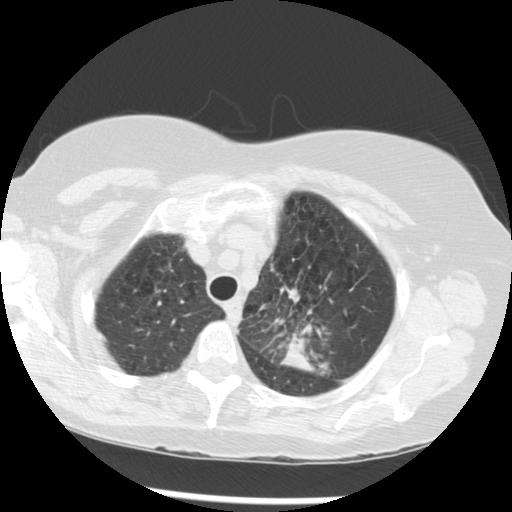
Low-dose screening chest CT, axial slice. Third annual screen. Lung window (W 1500 / L -600 HU). Slice 233 of 283 in the series. Female participant, aged 70 years at enrolment. Current smoker at enrolment.
Expert-annotated lung lesion, bounding box <253,283,350,371> (left, top, right, bottom; pixels). The exam's reader record, not a measurement of the box and not confirmed to be the same lesion: non-calcified nodule or mass ≥4 mm, left upper lobe, 32 × 26 mm, spiculated (stellate) margins, soft tissue attenuation, pre-existing on the prior screen: yes; interval growth: yes. Official screen result: positive, other. Participant outcome: lung cancer diagnosed 24 days after this screen — neoplasm, malignant, left upper lobe, stage IIIB (AJCC 6th edition), 40 mm at pathology.